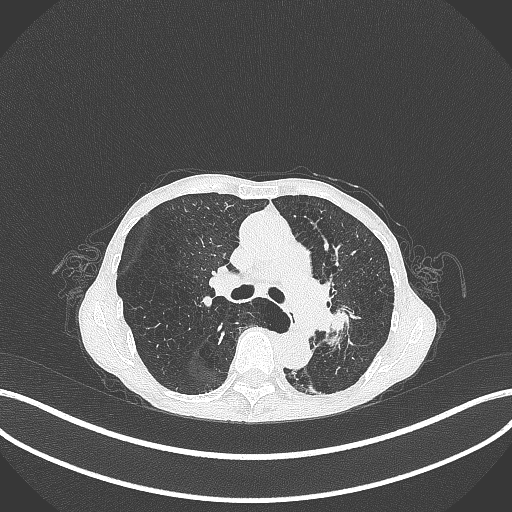
Chest CT, one axial slice; slice 175 of 347 in the series (ordered by position); lung window (W 1500 / L -600 HU); 1 mm slice thickness; 512 × 512 image matrix, field of view 400 × 400 mm. Female patient, age 70 years. From the clinical record (not read from this slice): clinical TNM (as recorded): T3 N0 M0; histopathological grade: G3.
Outlined on this slice (bounding box drawn by a radiologist):
- lung tumour (recorded histology: small cell carcinoma): bounding box (x1, y1, x2, y2) in pixels: (327, 305, 361, 339)